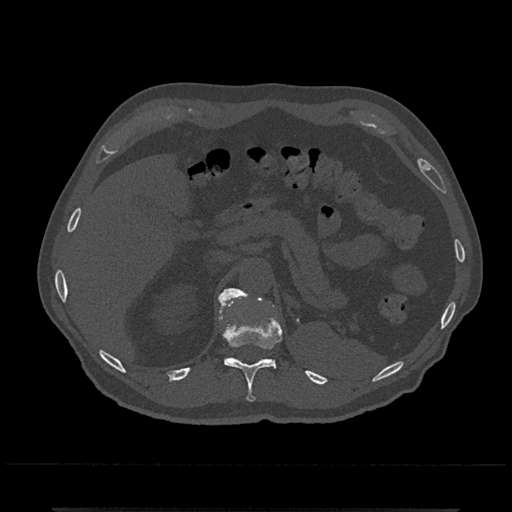
CT including the spine, one axial slice. Slice 476 of 797 in the series (ordered by position). 120 kVp. Bone window (W 1800 / L 400 HU). 512 × 512 image matrix, field of view 393 × 393 mm. Male patient, age 67 years. Case-level facts recorded for this patient, not image findings: primary cancer: prostate.
Structures marked on this image (semi-automatically segmented with operator editing):
- T11 vertebra: box from (x=219, y=297) to (x=282, y=402) px
- T12 vertebra: (x=220, y=288)–(x=262, y=307)